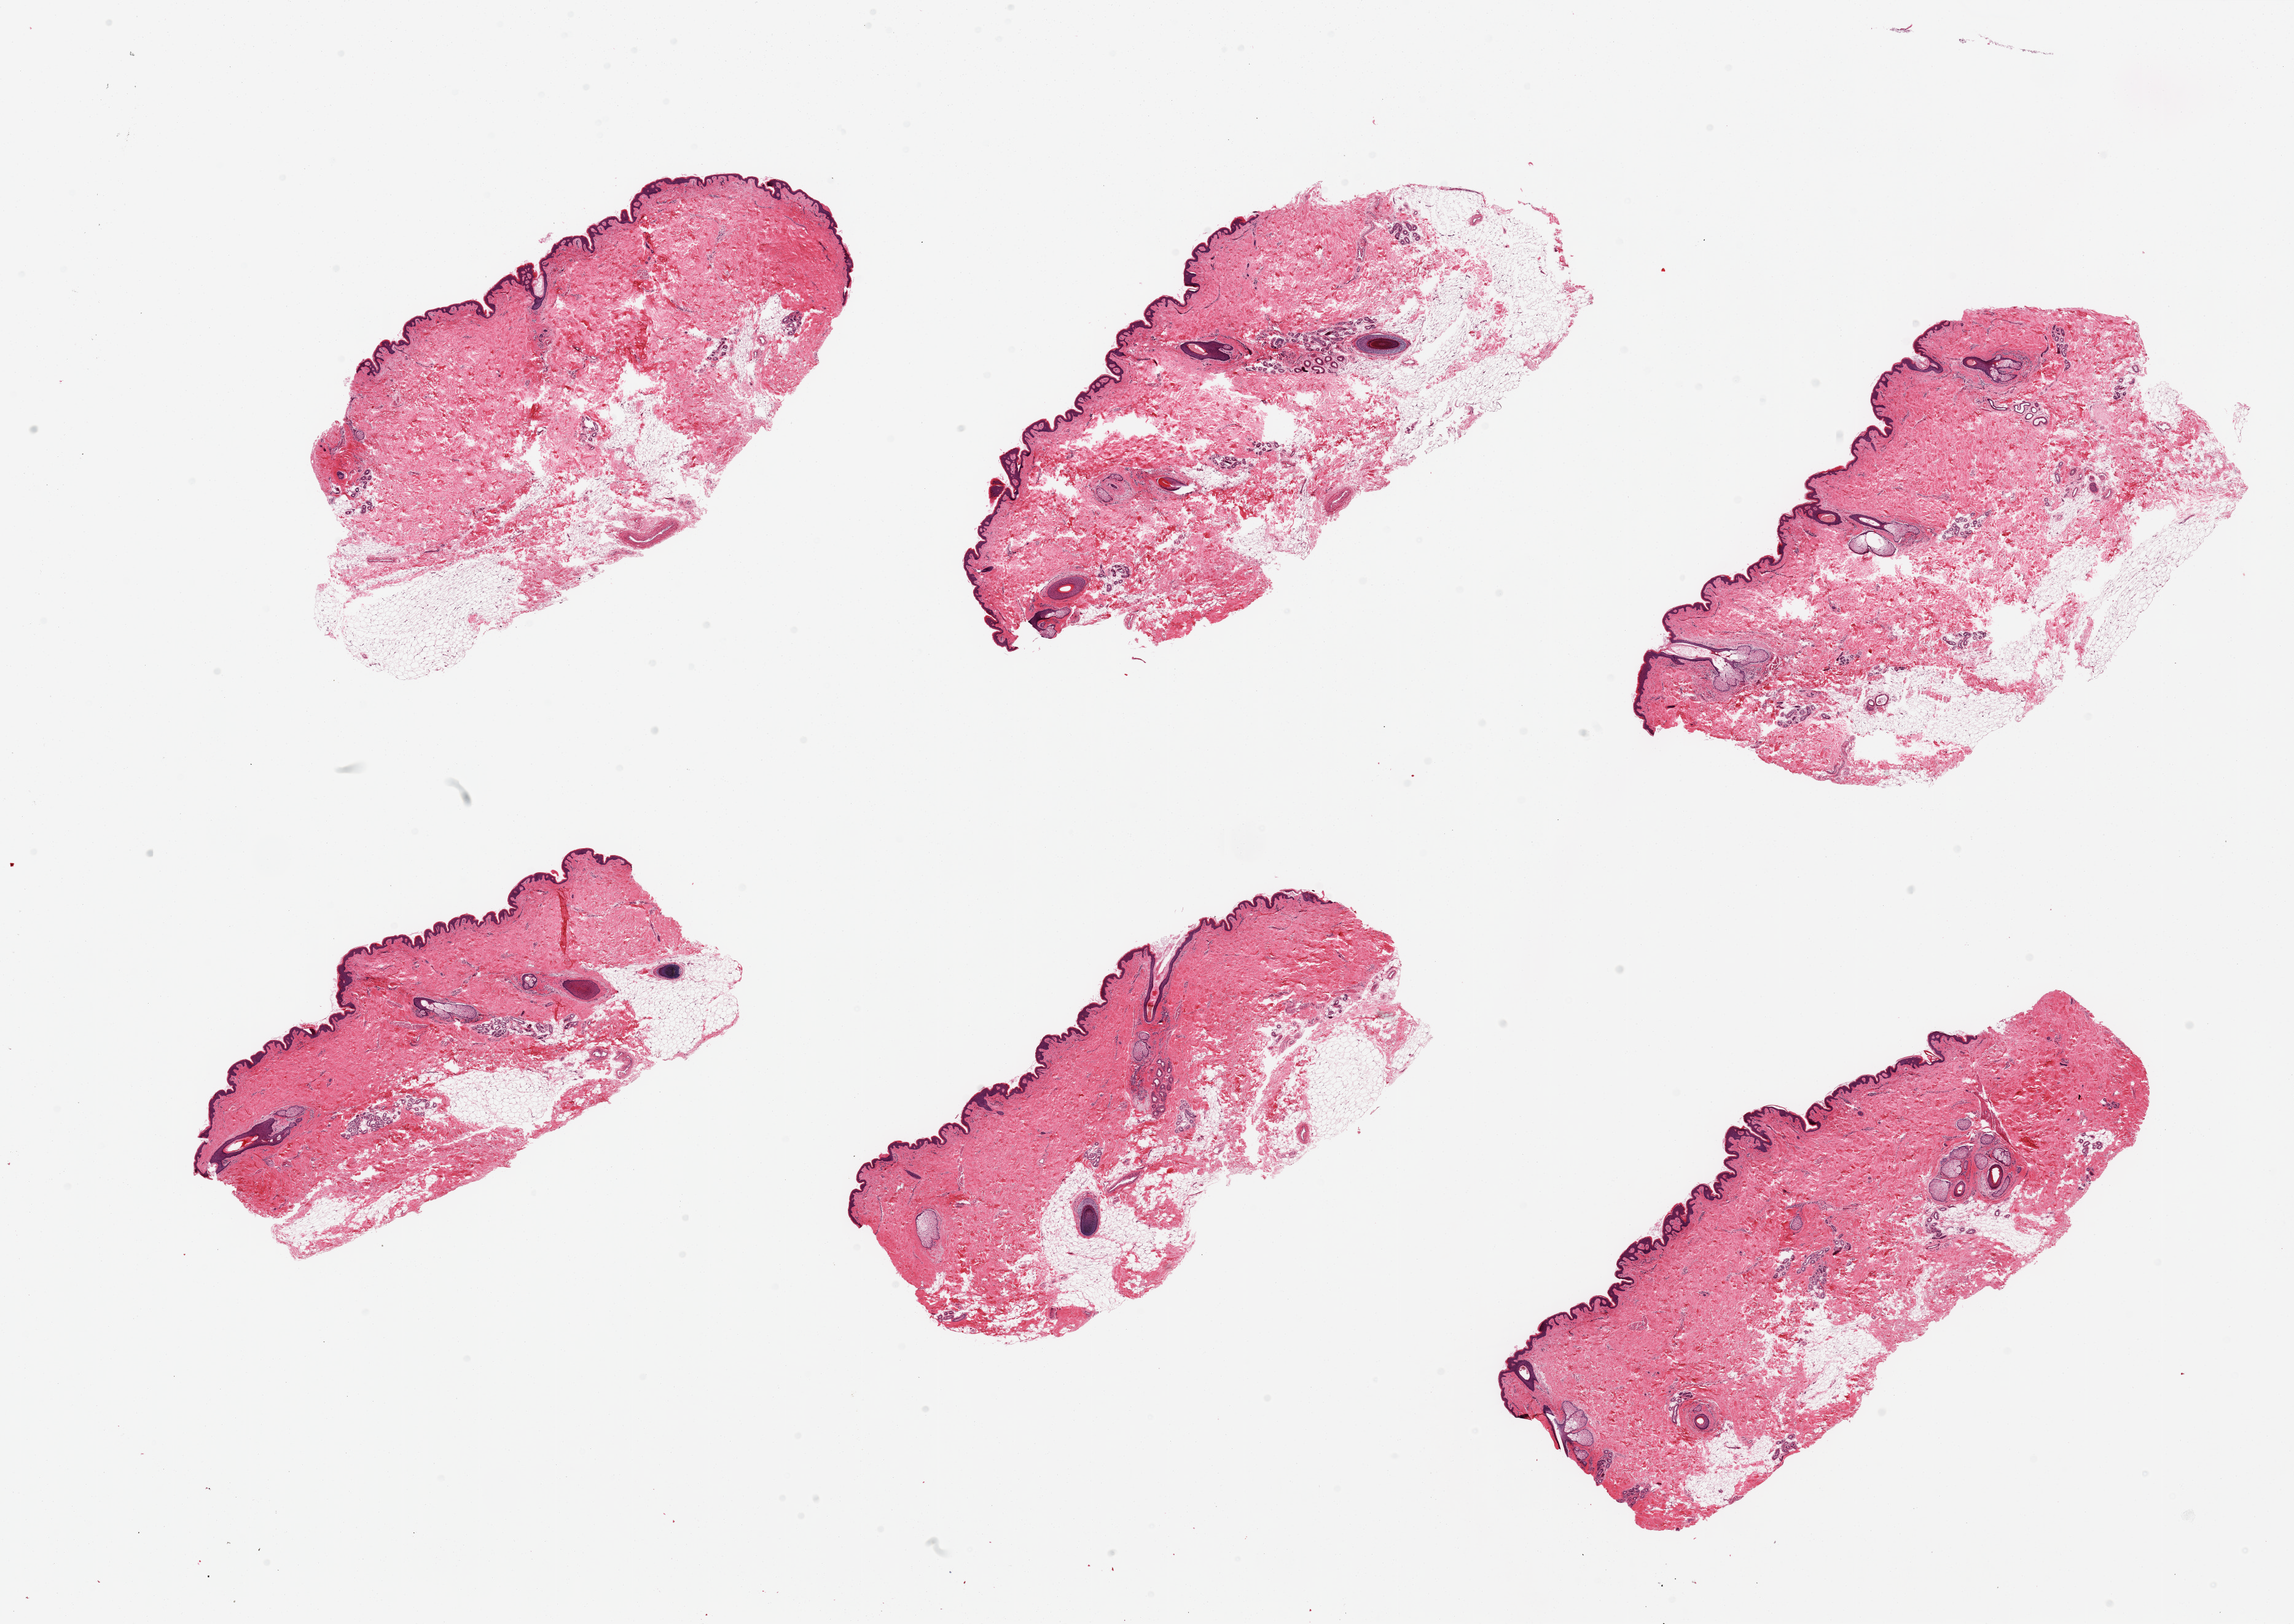
Whole-slide image, haematoxylin and eosin stain, shown as a low-resolution overview of the whole scanned area (about 29.5 x 20.9 mm), PAXgene-fixed paraffin-embedded (PFPE) section, section of skin of suprapubic region (target tissue), donor tissue sample. Male donor.
• review note (as recorded): 6 pieces; up to 20% dermal fat